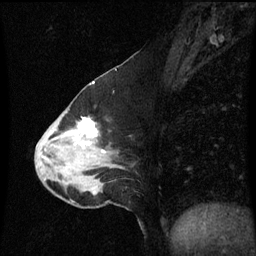
Breast MRI (dynamic contrast-enhanced), one sagittal slice. Slice 28 of 60 in the series (ordered by position). Dynamic contrast-enhanced series, image 2 of 3 at this slice position (ordered by acquisition). 1.5 T. TE 4.2 ms, TR 8.9 ms. 2 mm slice thickness. 256 × 256 image matrix, field of view 200 × 200 mm. Female patient, age 50 years. From the clinical record (not read from this slice): setting: breast cancer imaged before/during neoadjuvant chemotherapy; receptor status: HR-positive, HER2-negative.
Structures marked on this image (semi-automatically segmented with operator editing):
- analysis volume of interest (the breast-tissue region the enhancement analysis was run in; not a lesion): bounding box (x1, y1, x2, y2) in pixels: (36, 90, 123, 209)
- tumour enhancement mask (voxels above the 70 % enhancement threshold inside the analysis volume of interest): (52, 118, 98, 147)